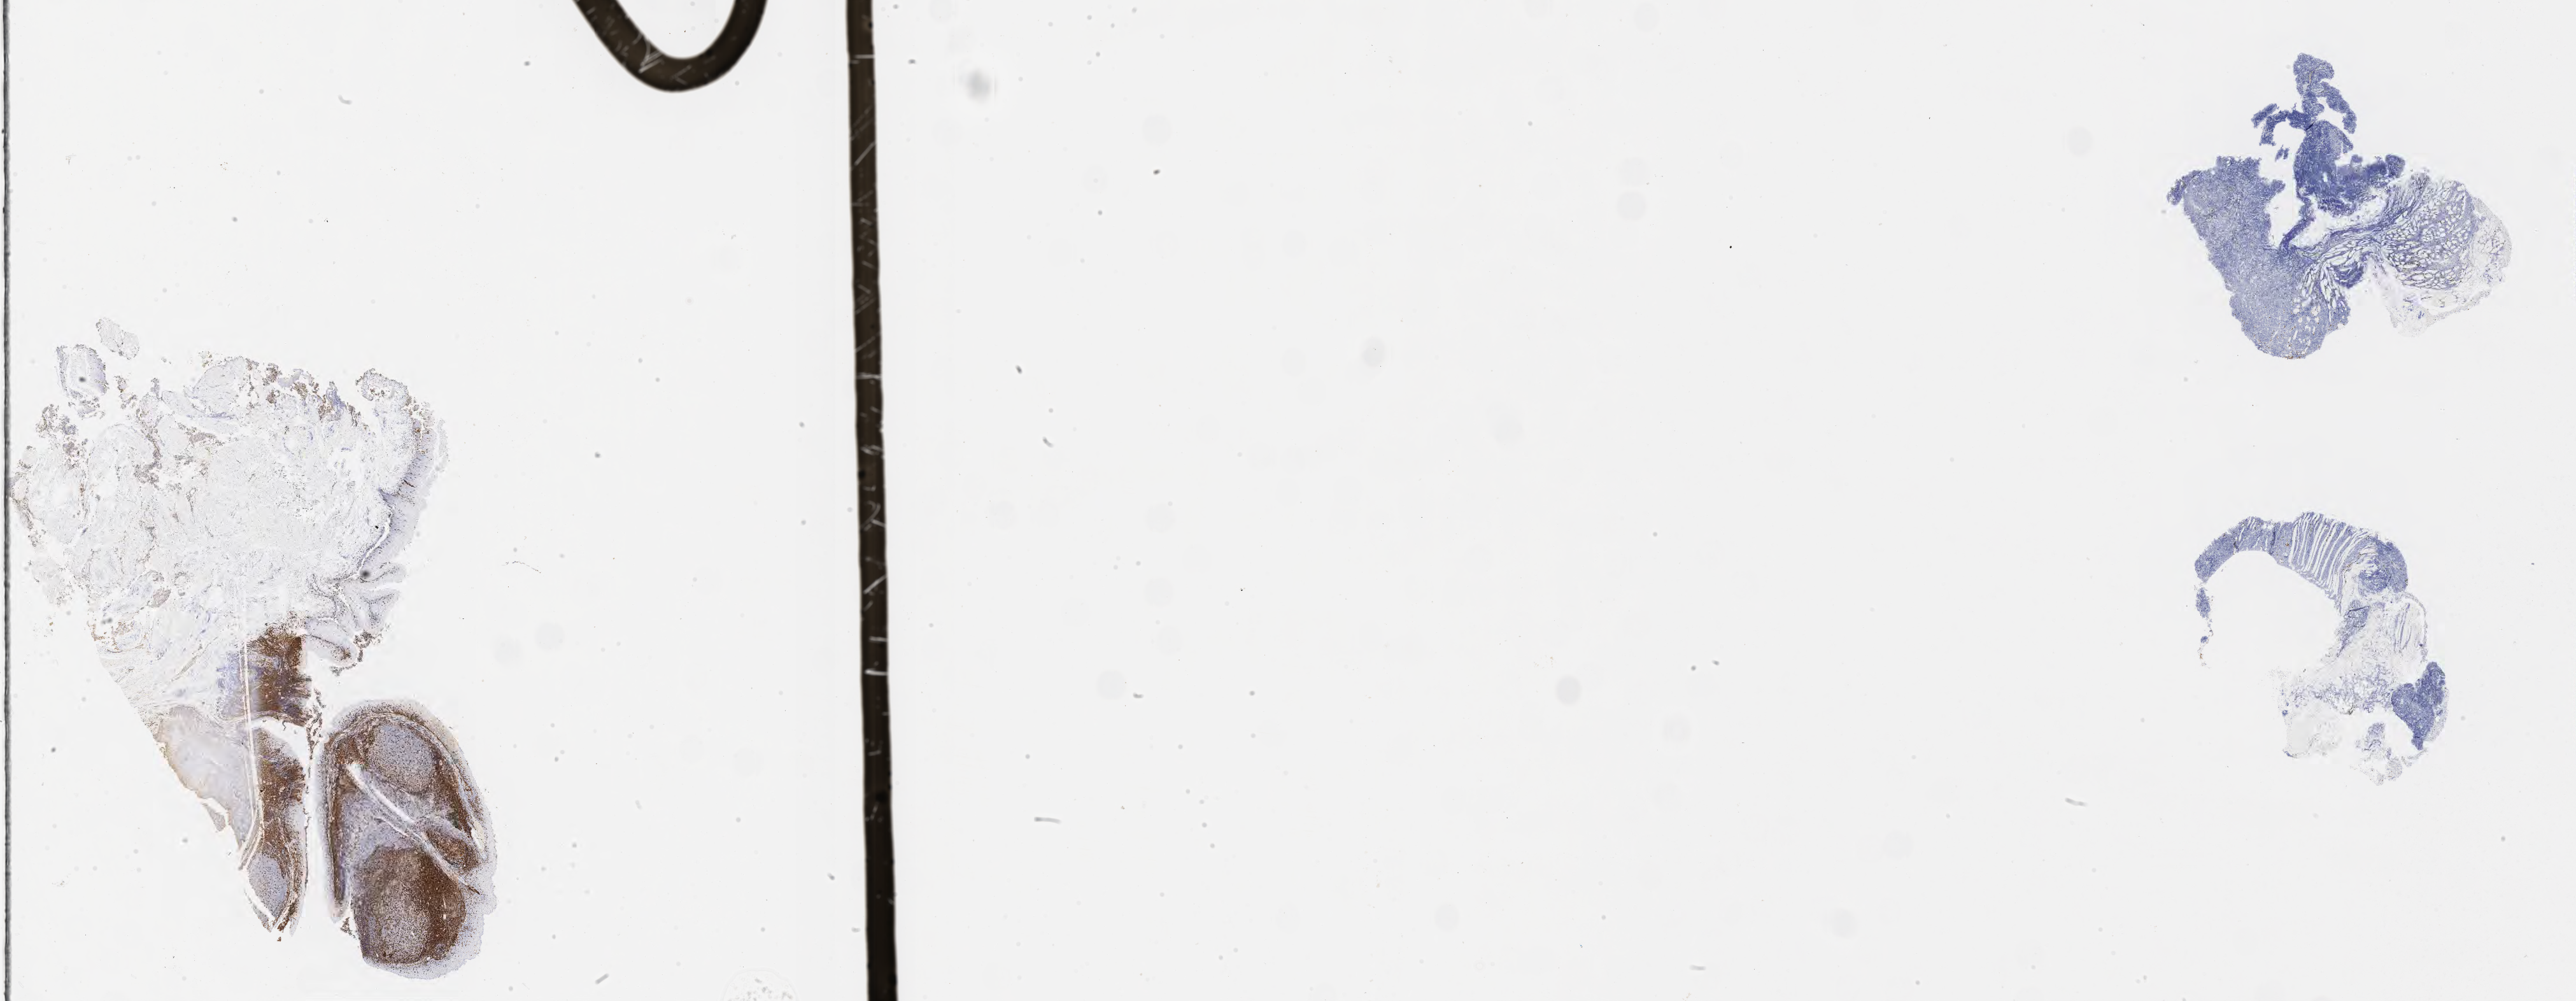
Whole-slide image, immunohistochemical stain for CD3, shown as a low-resolution overview of the whole scanned area (about 32.7 x 12.7 mm). Tumor tissue. Site: lymph node of head and neck. Patient male; age 73 years.
• histologic diagnosis: Burkitt lymphoma, NOS